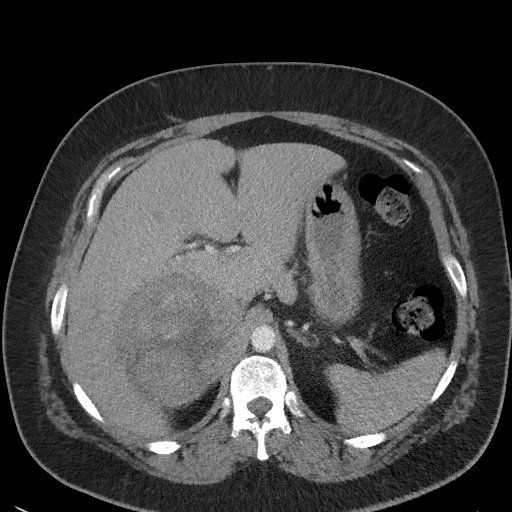
Contrast-enhanced abdominal CT, one axial slice. Slice 36 of 56 in the series (ordered by position). Soft-tissue window (W 400 / L 40 HU). 5 mm slice thickness. 512 × 512 image matrix, field of view 373 × 373 mm. Female patient, age 35 years. Case-level facts recorded for this patient, not image findings: diagnosis: adrenocortical carcinoma; tumour side: right adrenal; tumour size at pathology: 15 cm; Ki-67 index: 40 %; stage (as recorded): 2.
Outlined on this slice (semi-automatic segmentation, software-assisted and operator-edited):
- mass: box from (x=121, y=275) to (x=240, y=405) px